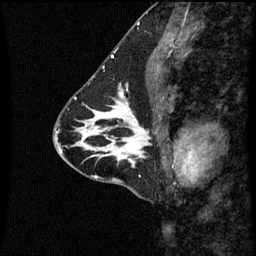
Breast MRI (dynamic contrast-enhanced), one sagittal slice; slice 28 of 60 in the series (ordered by position); dynamic contrast-enhanced series, image 2 of 3 at this slice position (ordered by acquisition); 1.5 T; TE 4.2 ms, TR 8.9 ms; 256 × 256 image matrix, field of view 200 × 200 mm. Patient: female, 43 years. Case-level facts recorded for this patient, not image findings: setting: breast cancer imaged before/during neoadjuvant chemotherapy; receptor status: HR-positive, HER2-negative.
Outlined on this slice (semi-automatic segmentation, software-assisted and operator-edited):
- analysis volume of interest (the breast-tissue region the enhancement analysis was run in; not a lesion): bounding box (x1, y1, x2, y2) in pixels: (110, 100, 166, 163)
- tumour enhancement mask (voxels above the 70 % enhancement threshold inside the analysis volume of interest): (113, 102, 143, 163)